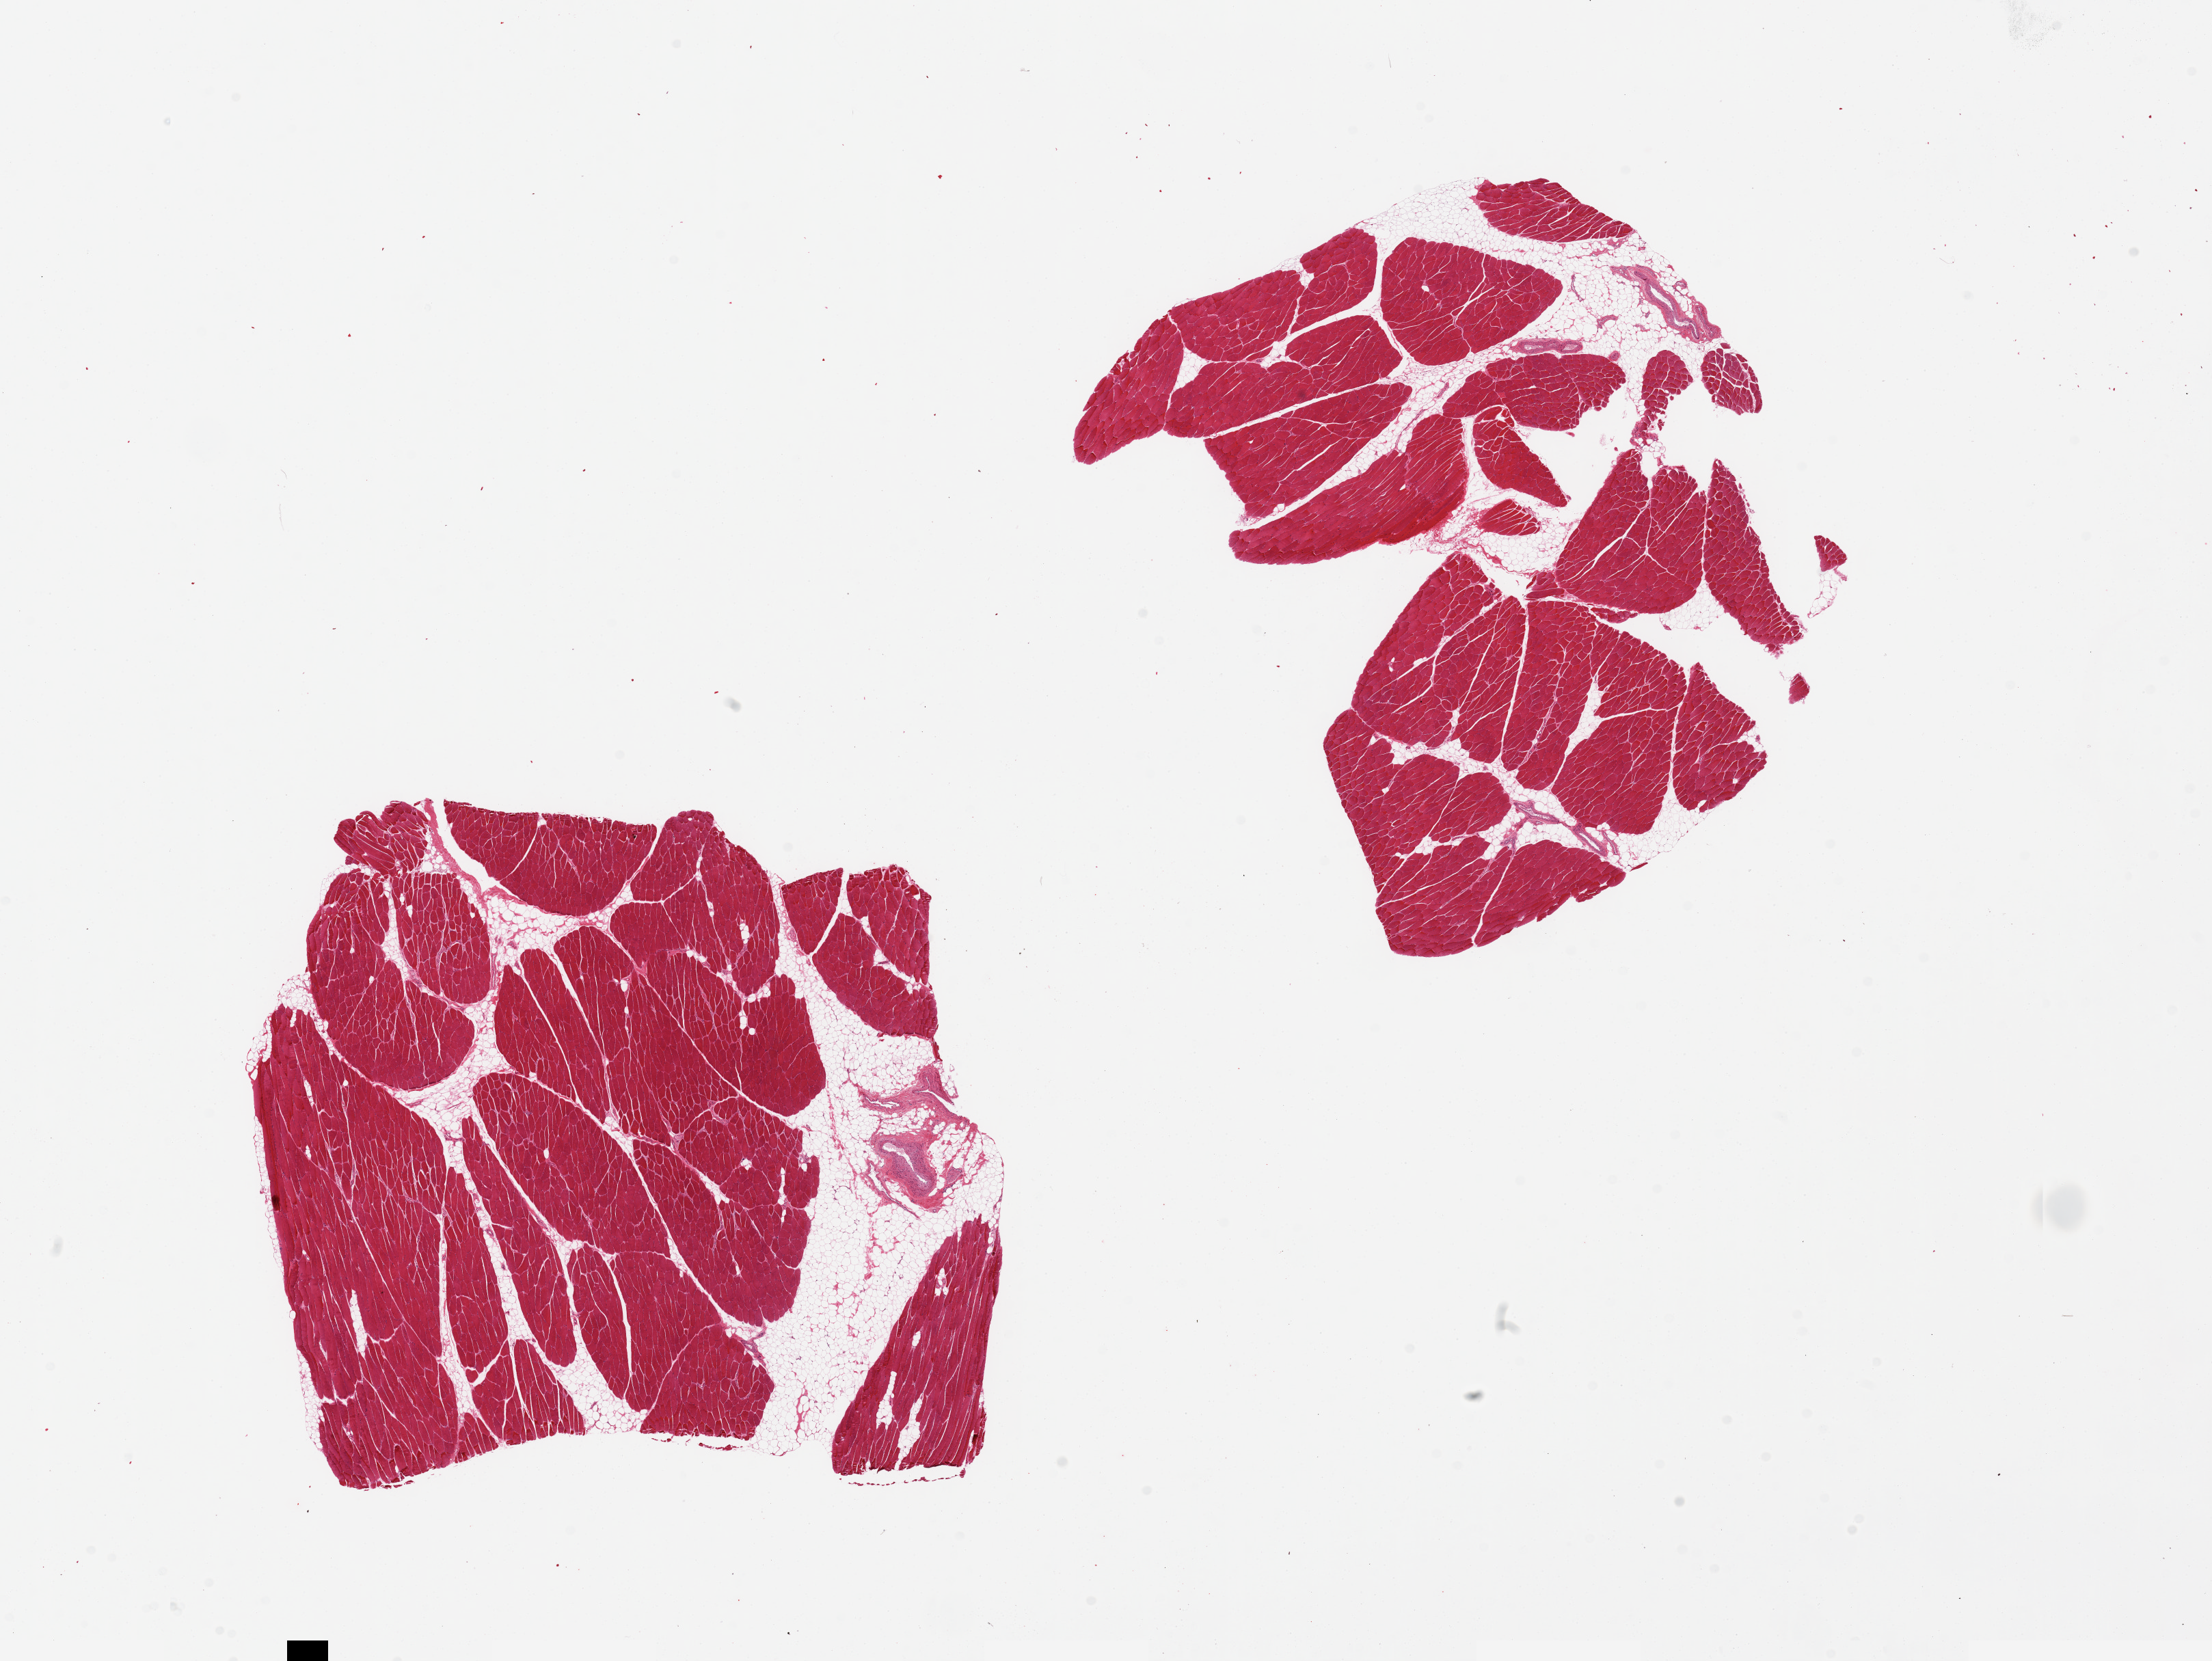
Digitized haematoxylin and eosin-stained section, brightfield — low-resolution overview of the scanned area, about 25.6 x 19.2 mm, PAXgene-fixed, paraffin-embedded tissue, sampled site (target tissue): skeletal muscle, donor tissue sample. Donor: male.
Reviewer comment on this tissue sample: 2 pieces, ~20% interstitial fat.